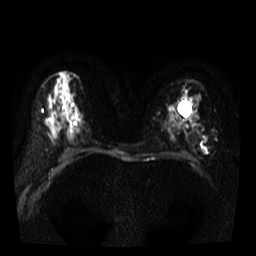
Breast MRI, one axial slice; position 22 of 38 along the scan axis; diffusion-weighted series; image 2 of 4 stored at this slice position (different b-values; order by instance number); 3 T; 5 mm slice thickness; 256 × 256 image matrix, field of view 320 × 320 mm. Female patient.
Structures marked on this image (outlined manually by an expert reader):
- tumour on diffusion-weighted imaging: box from (x=201, y=143) to (x=207, y=153) px